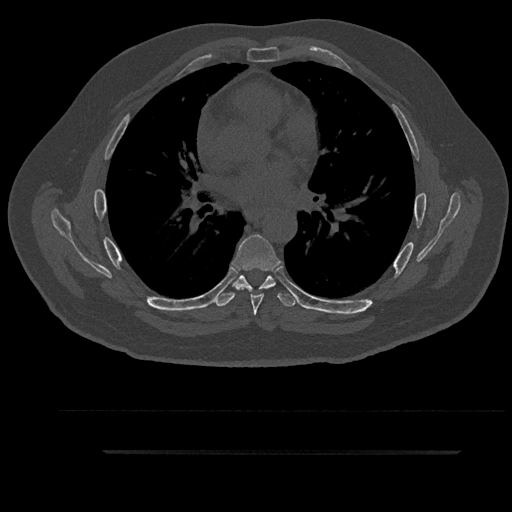
CT including the spine, one axial slice. Slice 557 of 797 in the series (ordered by position). Bone window (W 1800 / L 400 HU). 512 × 512 image matrix, field of view 432 × 432 mm. Male patient, age 63 years. Case-level facts recorded for this patient, not image findings: primary cancer: renal; vertebrae with lytic lesions (as recorded): T8.
Outlined on this slice (semi-automatically segmented with operator editing):
- T5 vertebra: box from (x=251, y=286) to (x=266, y=292) px
- T6 vertebra: (x=232, y=235)–(x=281, y=315)
- T7 vertebra: (x=215, y=275)–(x=298, y=307)